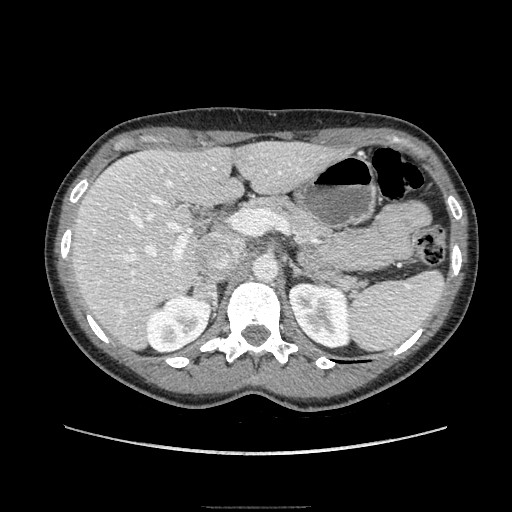
Contrast-enhanced abdominal CT, one axial slice; slice 111 of 193 in the series (ordered by position); soft-tissue window (W 400 / L 40 HU); 1.25 mm slice thickness; 512 × 512 image matrix, field of view 380 × 380 mm. Female patient. Case-level facts recorded for this patient, not image findings: diagnosis: adrenocortical carcinoma; tumour side: right adrenal; tumour size at pathology: 3 cm; Ki-67 index: 4 %; stage (as recorded): 1.
Outlined on this slice (semi-automatic segmentation, software-assisted and operator-edited):
- mass: bounding box (x1, y1, x2, y2) in pixels: (195, 277, 217, 306)